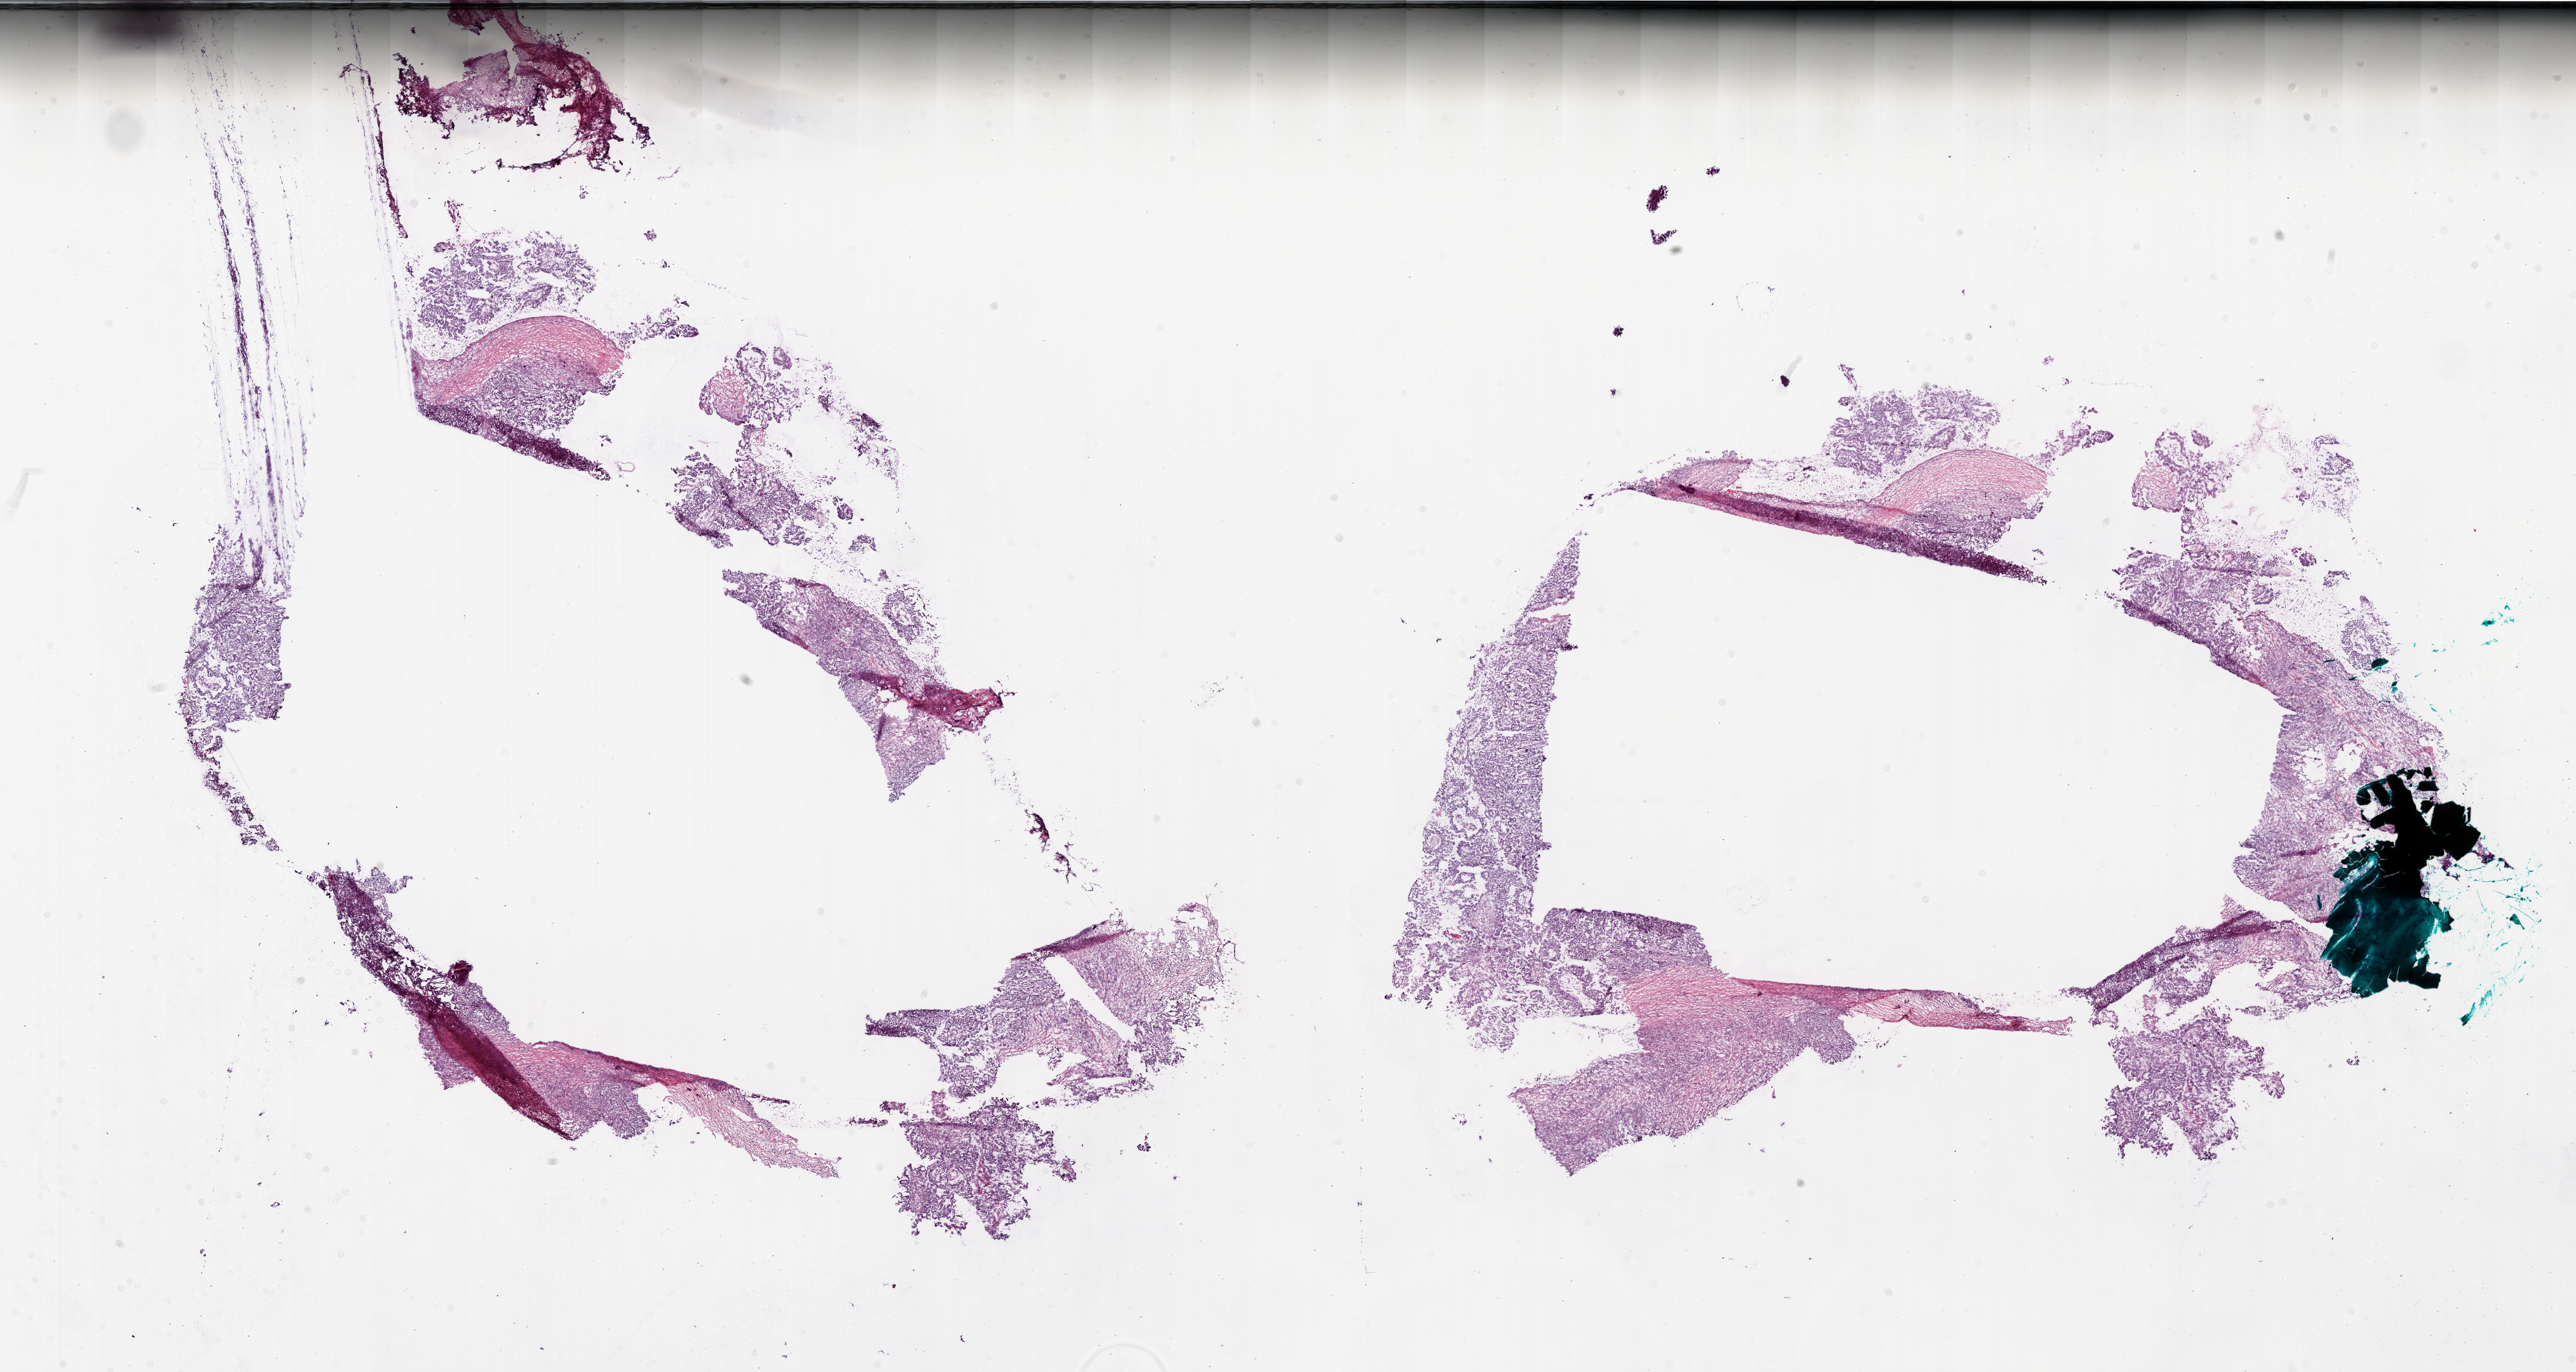
Digitized H&E-stained tissue section (whole slide) — low-resolution overview of the scanned area, about 33.0 x 17.6 mm (slide scanned at 20x). Frozen section from the bottom of the tissue portion. Primary tumour sample from the ovary. Female, age 75 years at initial diagnosis. Histologic grade: GX (grade cannot be assessed). Composition of this section per pathologist review: tumour cells 79%, tumour nuclei 80%, normal cells 20%, stromal cells 0%, necrosis 1%.
* FIGO stage: IV
* diagnosis: Serous cystadenocarcinoma, NOS